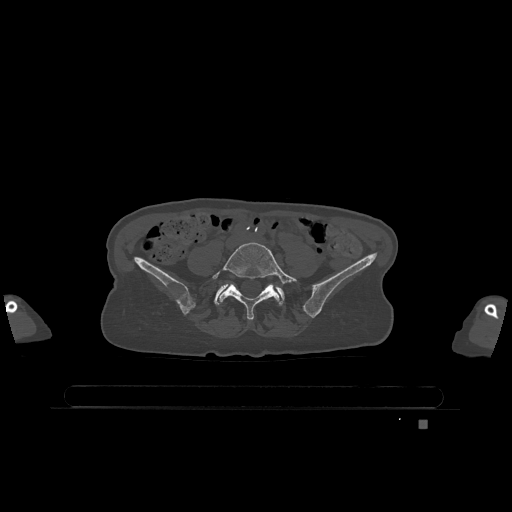
CT including the spine, one axial slice; slice 237 of 1317 in the series (ordered by position); bone window (W 1800 / L 400 HU); 512 × 512 image matrix, field of view 500 × 500 mm. Female patient, age 74 years. From the clinical record (not read from this slice): primary cancer: lung; vertebrae with lytic lesions (as recorded): T1, T4, T5, T6, L4, L5.
Annotated regions visible in this slice (semi-automatically segmented with operator editing):
- L5 vertebra: bounding box (x1, y1, x2, y2) in pixels: (212, 242, 297, 320)